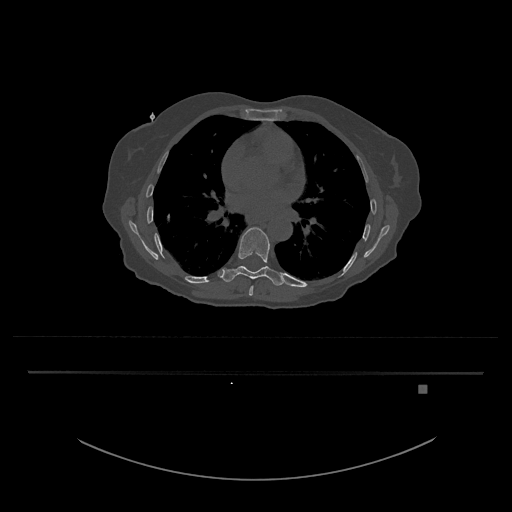
CT including the spine, one axial slice; position 764 of 797 along the scan axis; reconstruction kernel Br40s/3; 120 kVp; bone window (W 1800 / L 400 HU); 512 × 512 image matrix, field of view 500 × 500 mm. Female patient, age 57 years. Case-level facts recorded for this patient, not image findings: primary cancer: cervical.
Structures marked on this image (semi-automatically segmented with operator editing):
- T8 vertebra: bounding box <249,286,254,296> (left, top, right, bottom; pixels)
- T9 vertebra: <221,227,286,286>